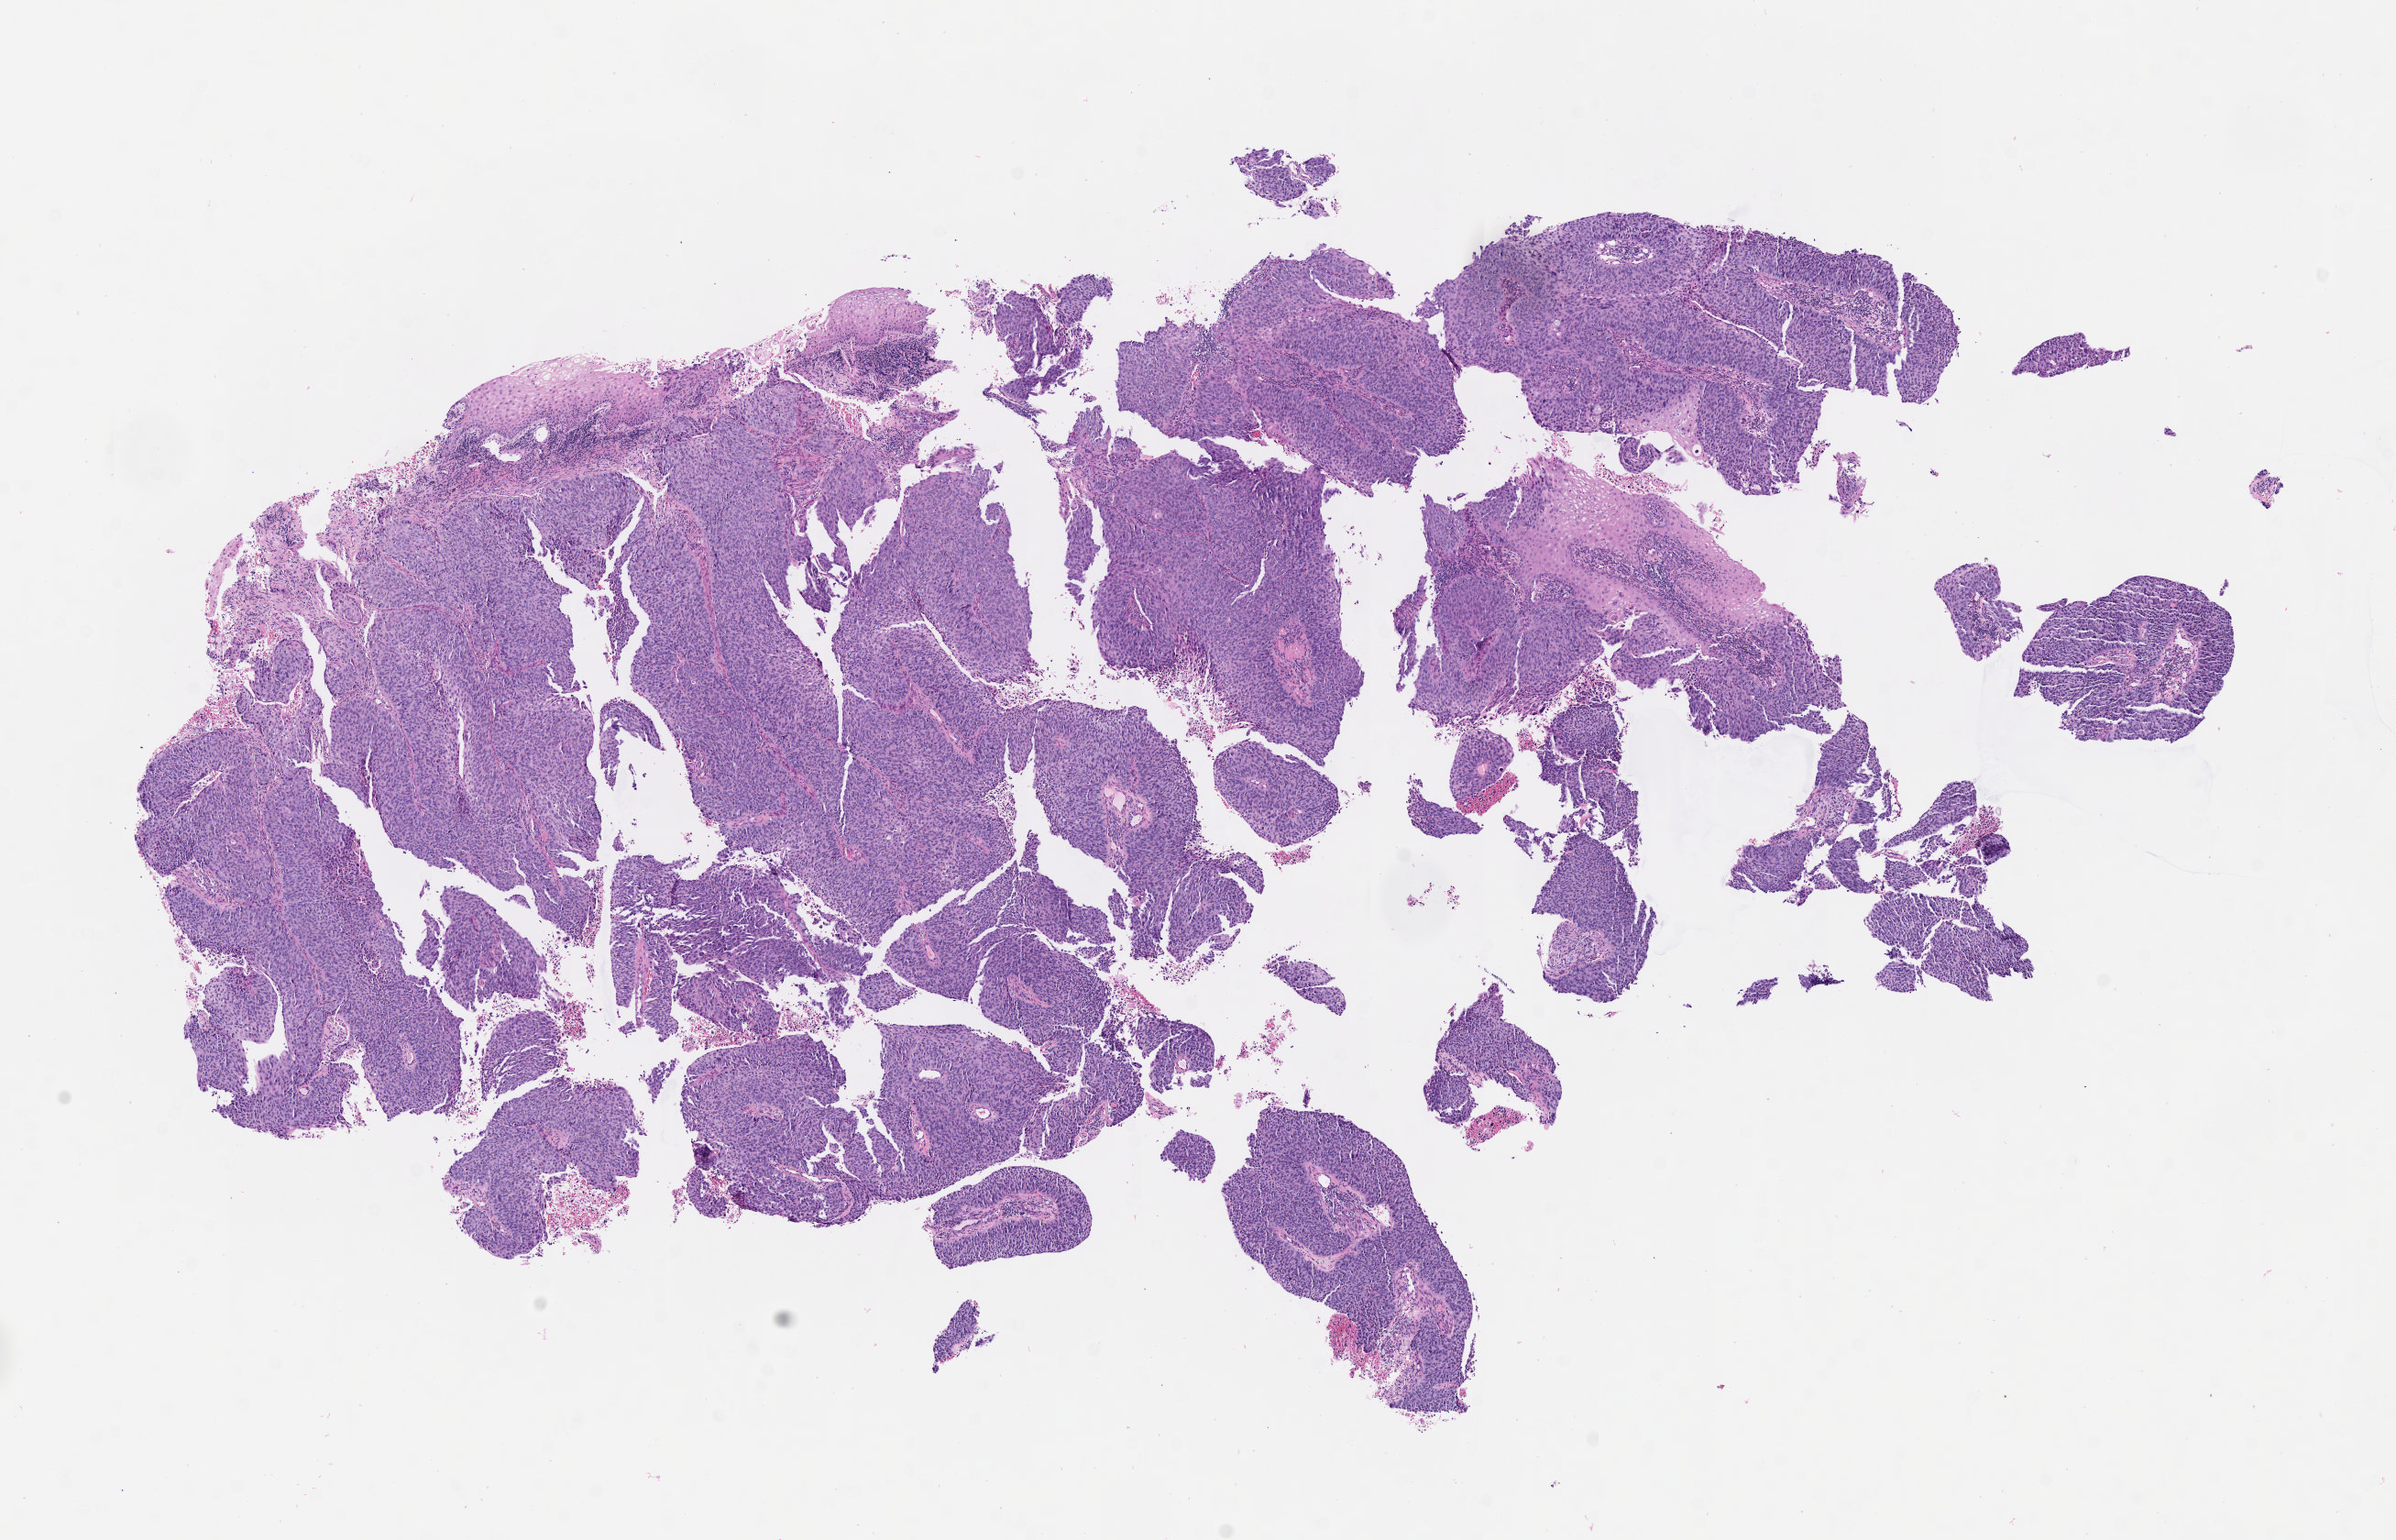
Whole-slide image, H&E stain — shown as a low-resolution overview of the whole scanned area (about 10.6 x 6.8 mm); tumor tissue; anatomic site: cervix. Female patient, aged 46.
Histologic diagnosis: Basaloid squamous cell carcinoma.